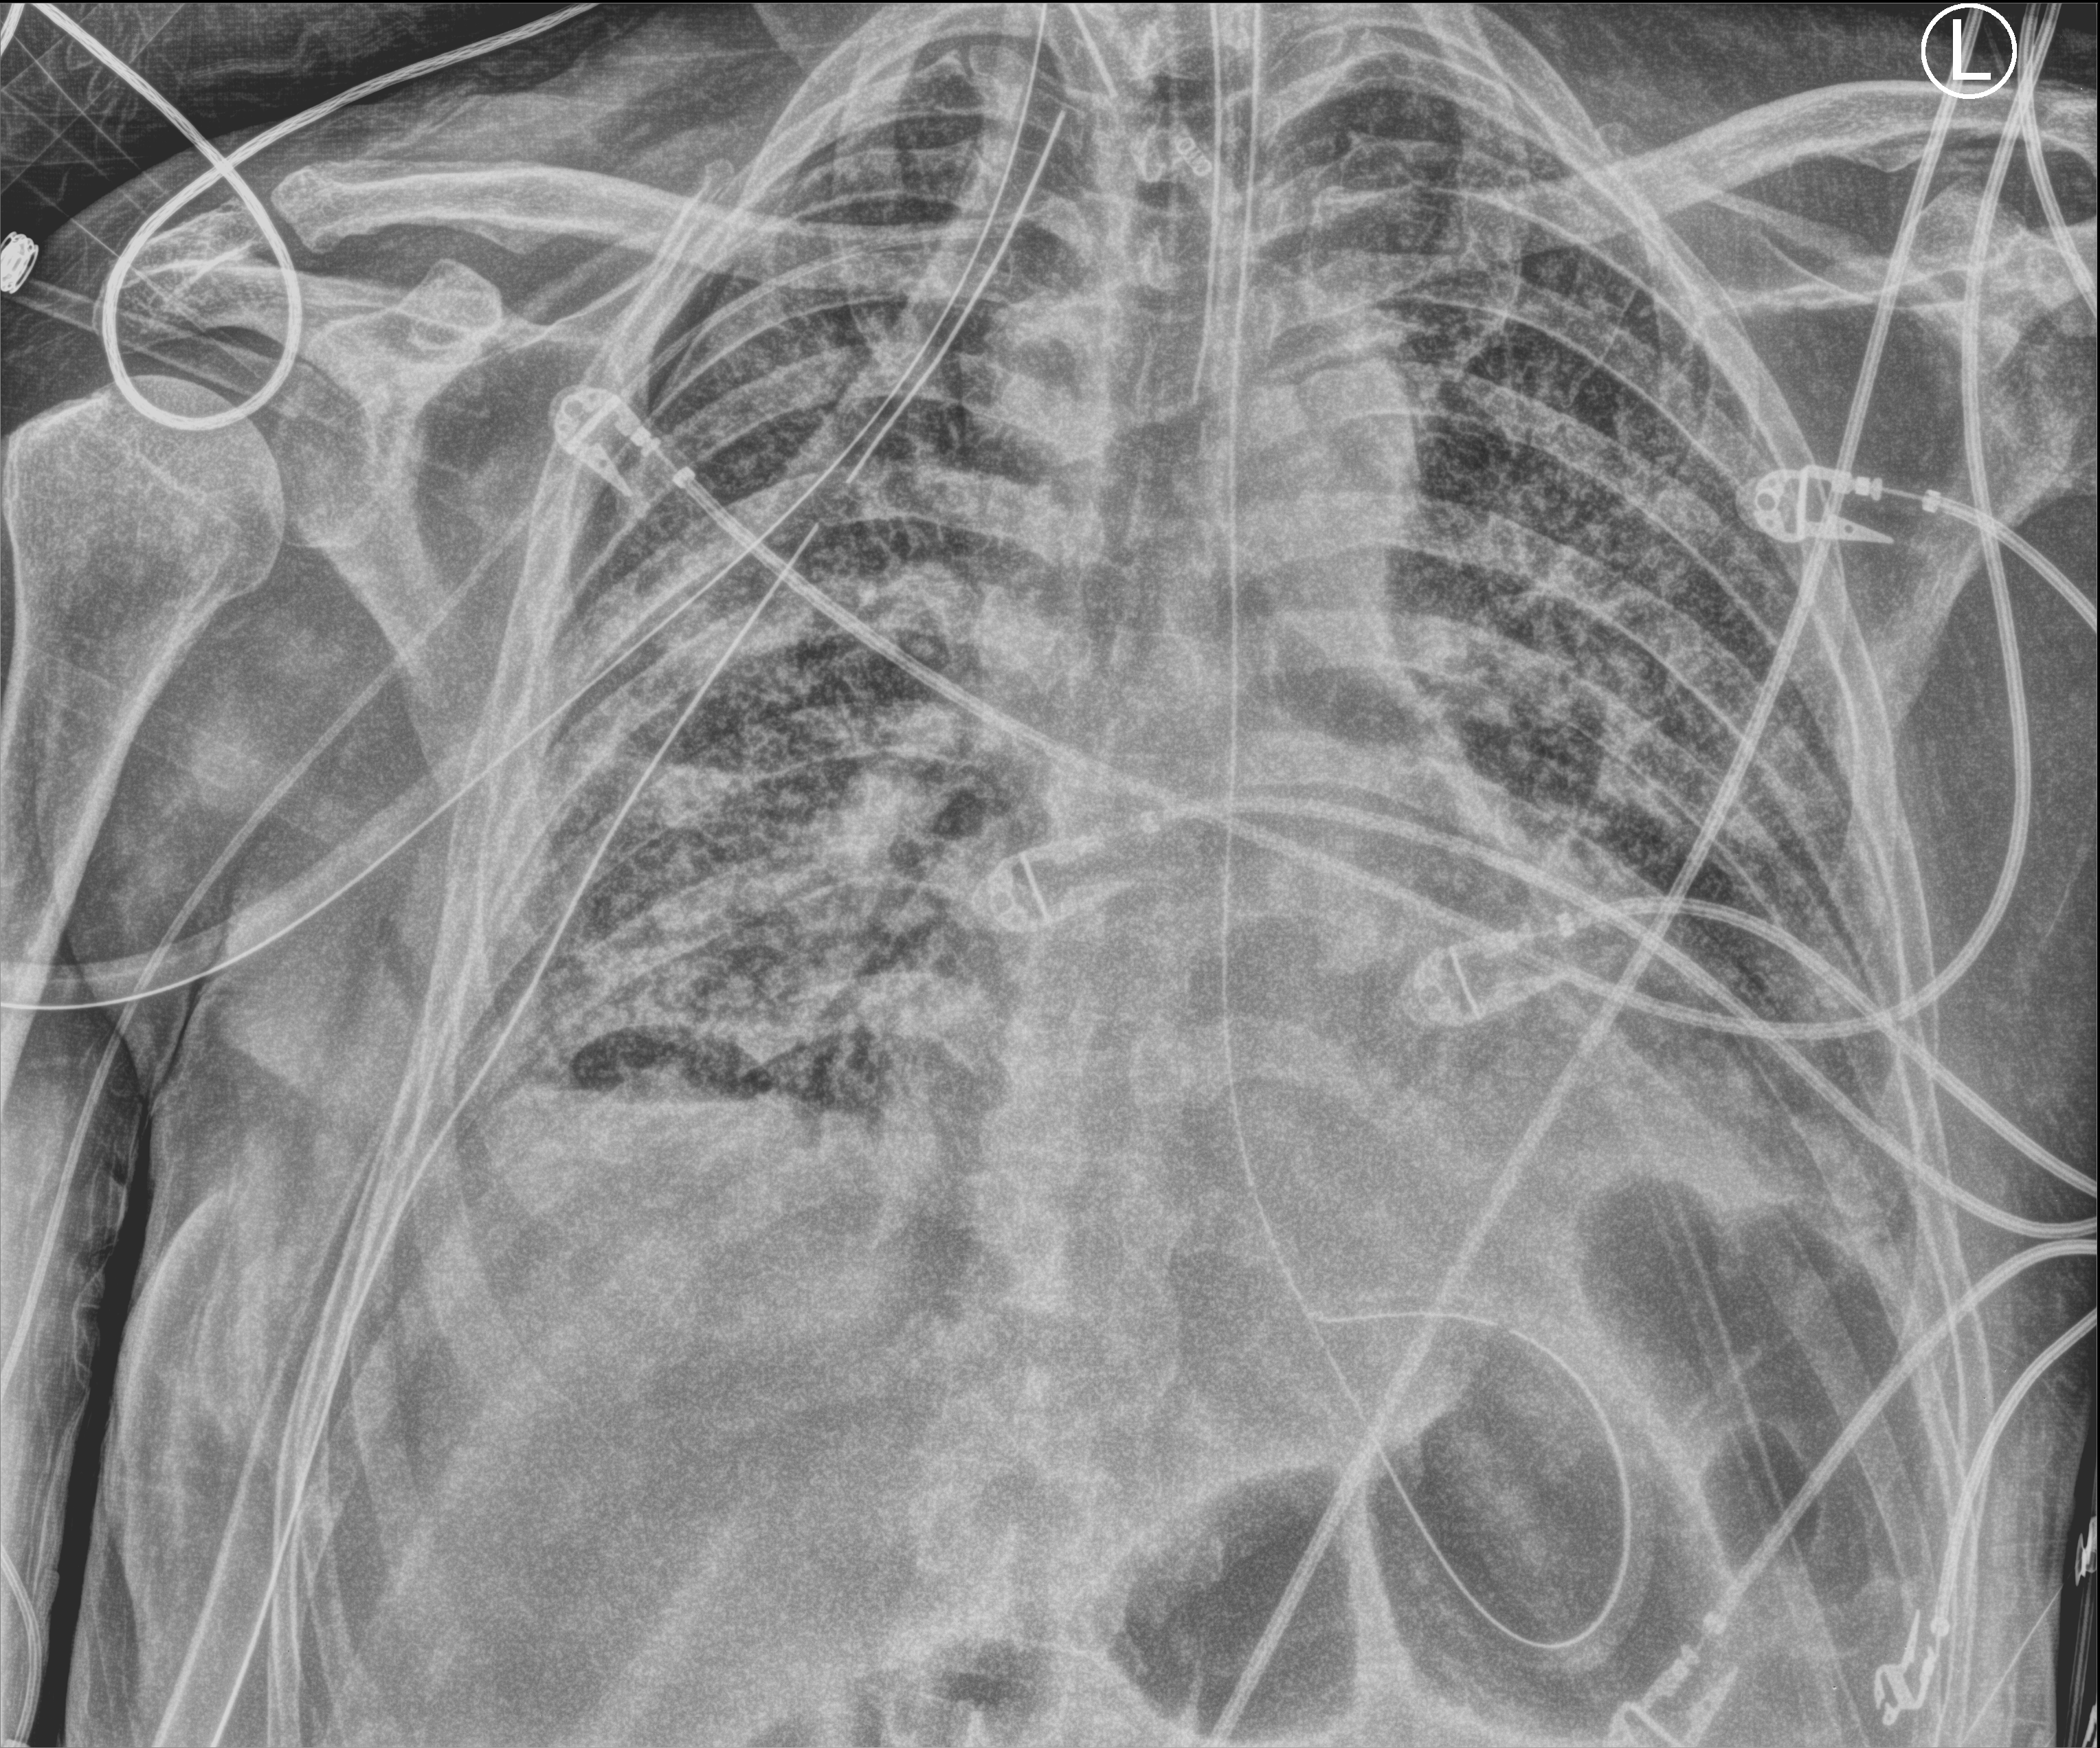
Portable chest radiograph, anteroposterior (AP) projection. Male patient hospitalised with COVID-19, age 60–74 years.
Admission-level facts for this patient (not findings on this image; timing relative to this image not recorded): length of hospital stay: 37 days; smoking status (admission record): never; mechanically ventilated during this hospital stay: yes.